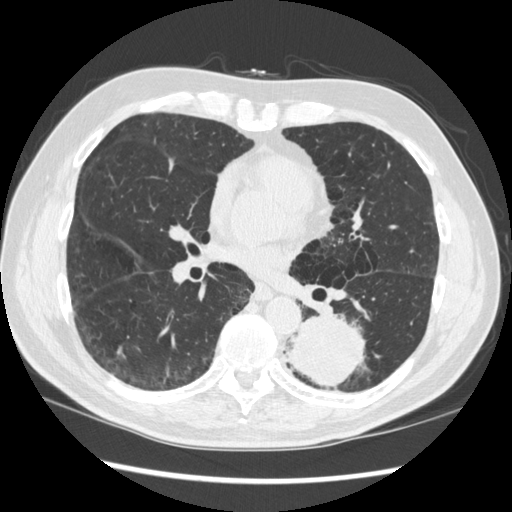
Low-dose screening chest CT, one axial slice. Reconstruction kernel STANDARD. 120 kVp. Lung window (W 1500 / L -600 HU). 512 × 512 image matrix.
Structures marked on this image (manually delineated by an expert):
- lesion 1 (tumor, lower lobe of left lung): bounding box (x1, y1, x2, y2) in pixels: (287, 315, 365, 388)